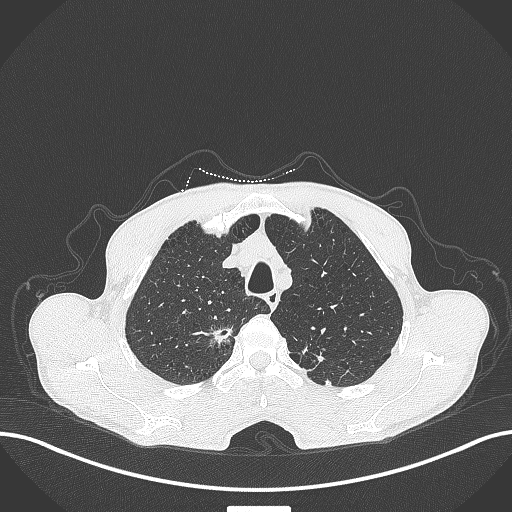
Chest CT, one axial slice. Position 353 of 445 along the scan axis. Reconstruction kernel B70f. 120 kVp. Lung window (W 1500 / L -600 HU). 512 × 512 image matrix. Patient: male, 70 years. Case-level facts recorded for this patient, not image findings: clinical TNM (as recorded): T1a N0 M0; histopathological grade: G1-2.
Structures marked on this image (bounding box drawn by a radiologist):
- lung tumour (recorded histology: adenocarcinoma): bounding box [x1, y1, x2, y2] px = [205, 319, 235, 346]